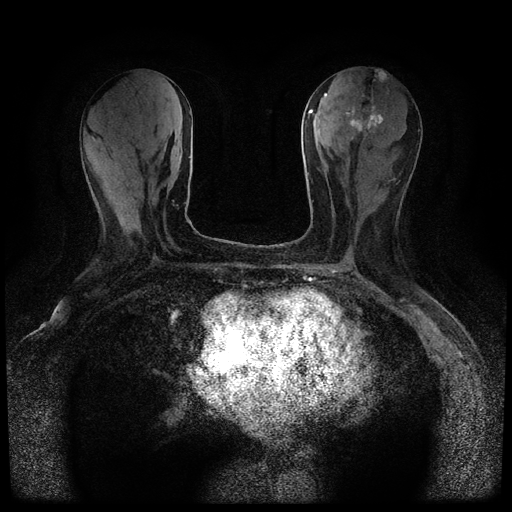
Breast MRI (dynamic contrast-enhanced, multi-phase), one axial slice; slice 31 of 116 in the series (ordered by position); dynamic contrast-enhanced series, time point 2 of 5 at this slice position (early post-contrast); 1.5 T; TE 2.7 ms, TR 5.4 ms; 512 × 512 image matrix, field of view 320 × 320 mm. Patient: female, 80 years.
Annotated regions visible in this slice (semi-automatic segmentation, software-assisted and operator-edited):
- breast lesion (labelled 'tumour' in the annotation; benign lesions carry a separate 'benign' label): bounding box (x1, y1, x2, y2) in pixels: (346, 70, 387, 136)